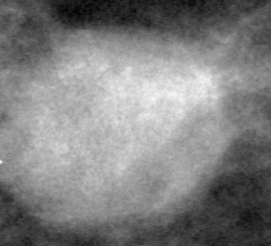
Region of interest cut from a scanned film mammogram (one marked finding); left breast; MLO view.
Finding: mass, shape round, margins obscured; BI-RADS assessment category 4; pathology result (as recorded, not read from the image): benign.